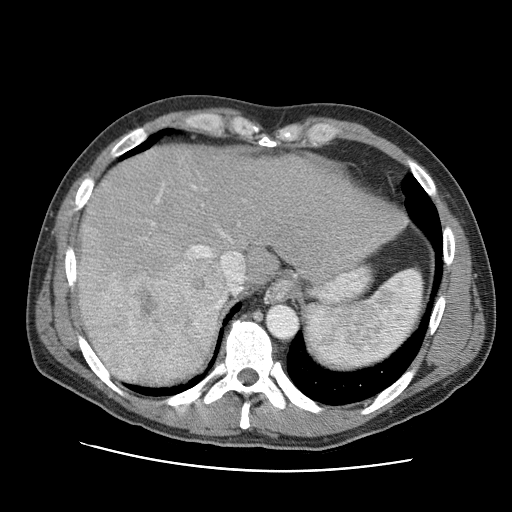
Contrast-enhanced abdominal CT (liver protocol), one axial slice. Slice 76 of 95 in the series (ordered by position). Reconstruction kernel STANDARD. One of 2 acquisitions stored at this slice position. Soft-tissue window (W 400 / L 40 HU). 2.5 mm slice thickness. 512 × 512 image matrix. Case-level facts recorded for this patient, not image findings: diagnosis: hepatocellular carcinoma (patient treated with transarterial chemoembolisation; whether this scan precedes or follows treatment is not stated here); TNM stage (as recorded): Stage-IVA; Child-Pugh class: A.
Annotated regions visible in this slice (semi-automatic segmentation, software-assisted and operator-edited):
- liver parenchyma outside the tumour (the mass and vessels are separate outlines, so this box may not span the whole liver): box from (x=76, y=146) to (x=406, y=378) px
- mass: (x=79, y=232)–(x=229, y=387)
- liver vessels: (x=144, y=185)–(x=244, y=291)